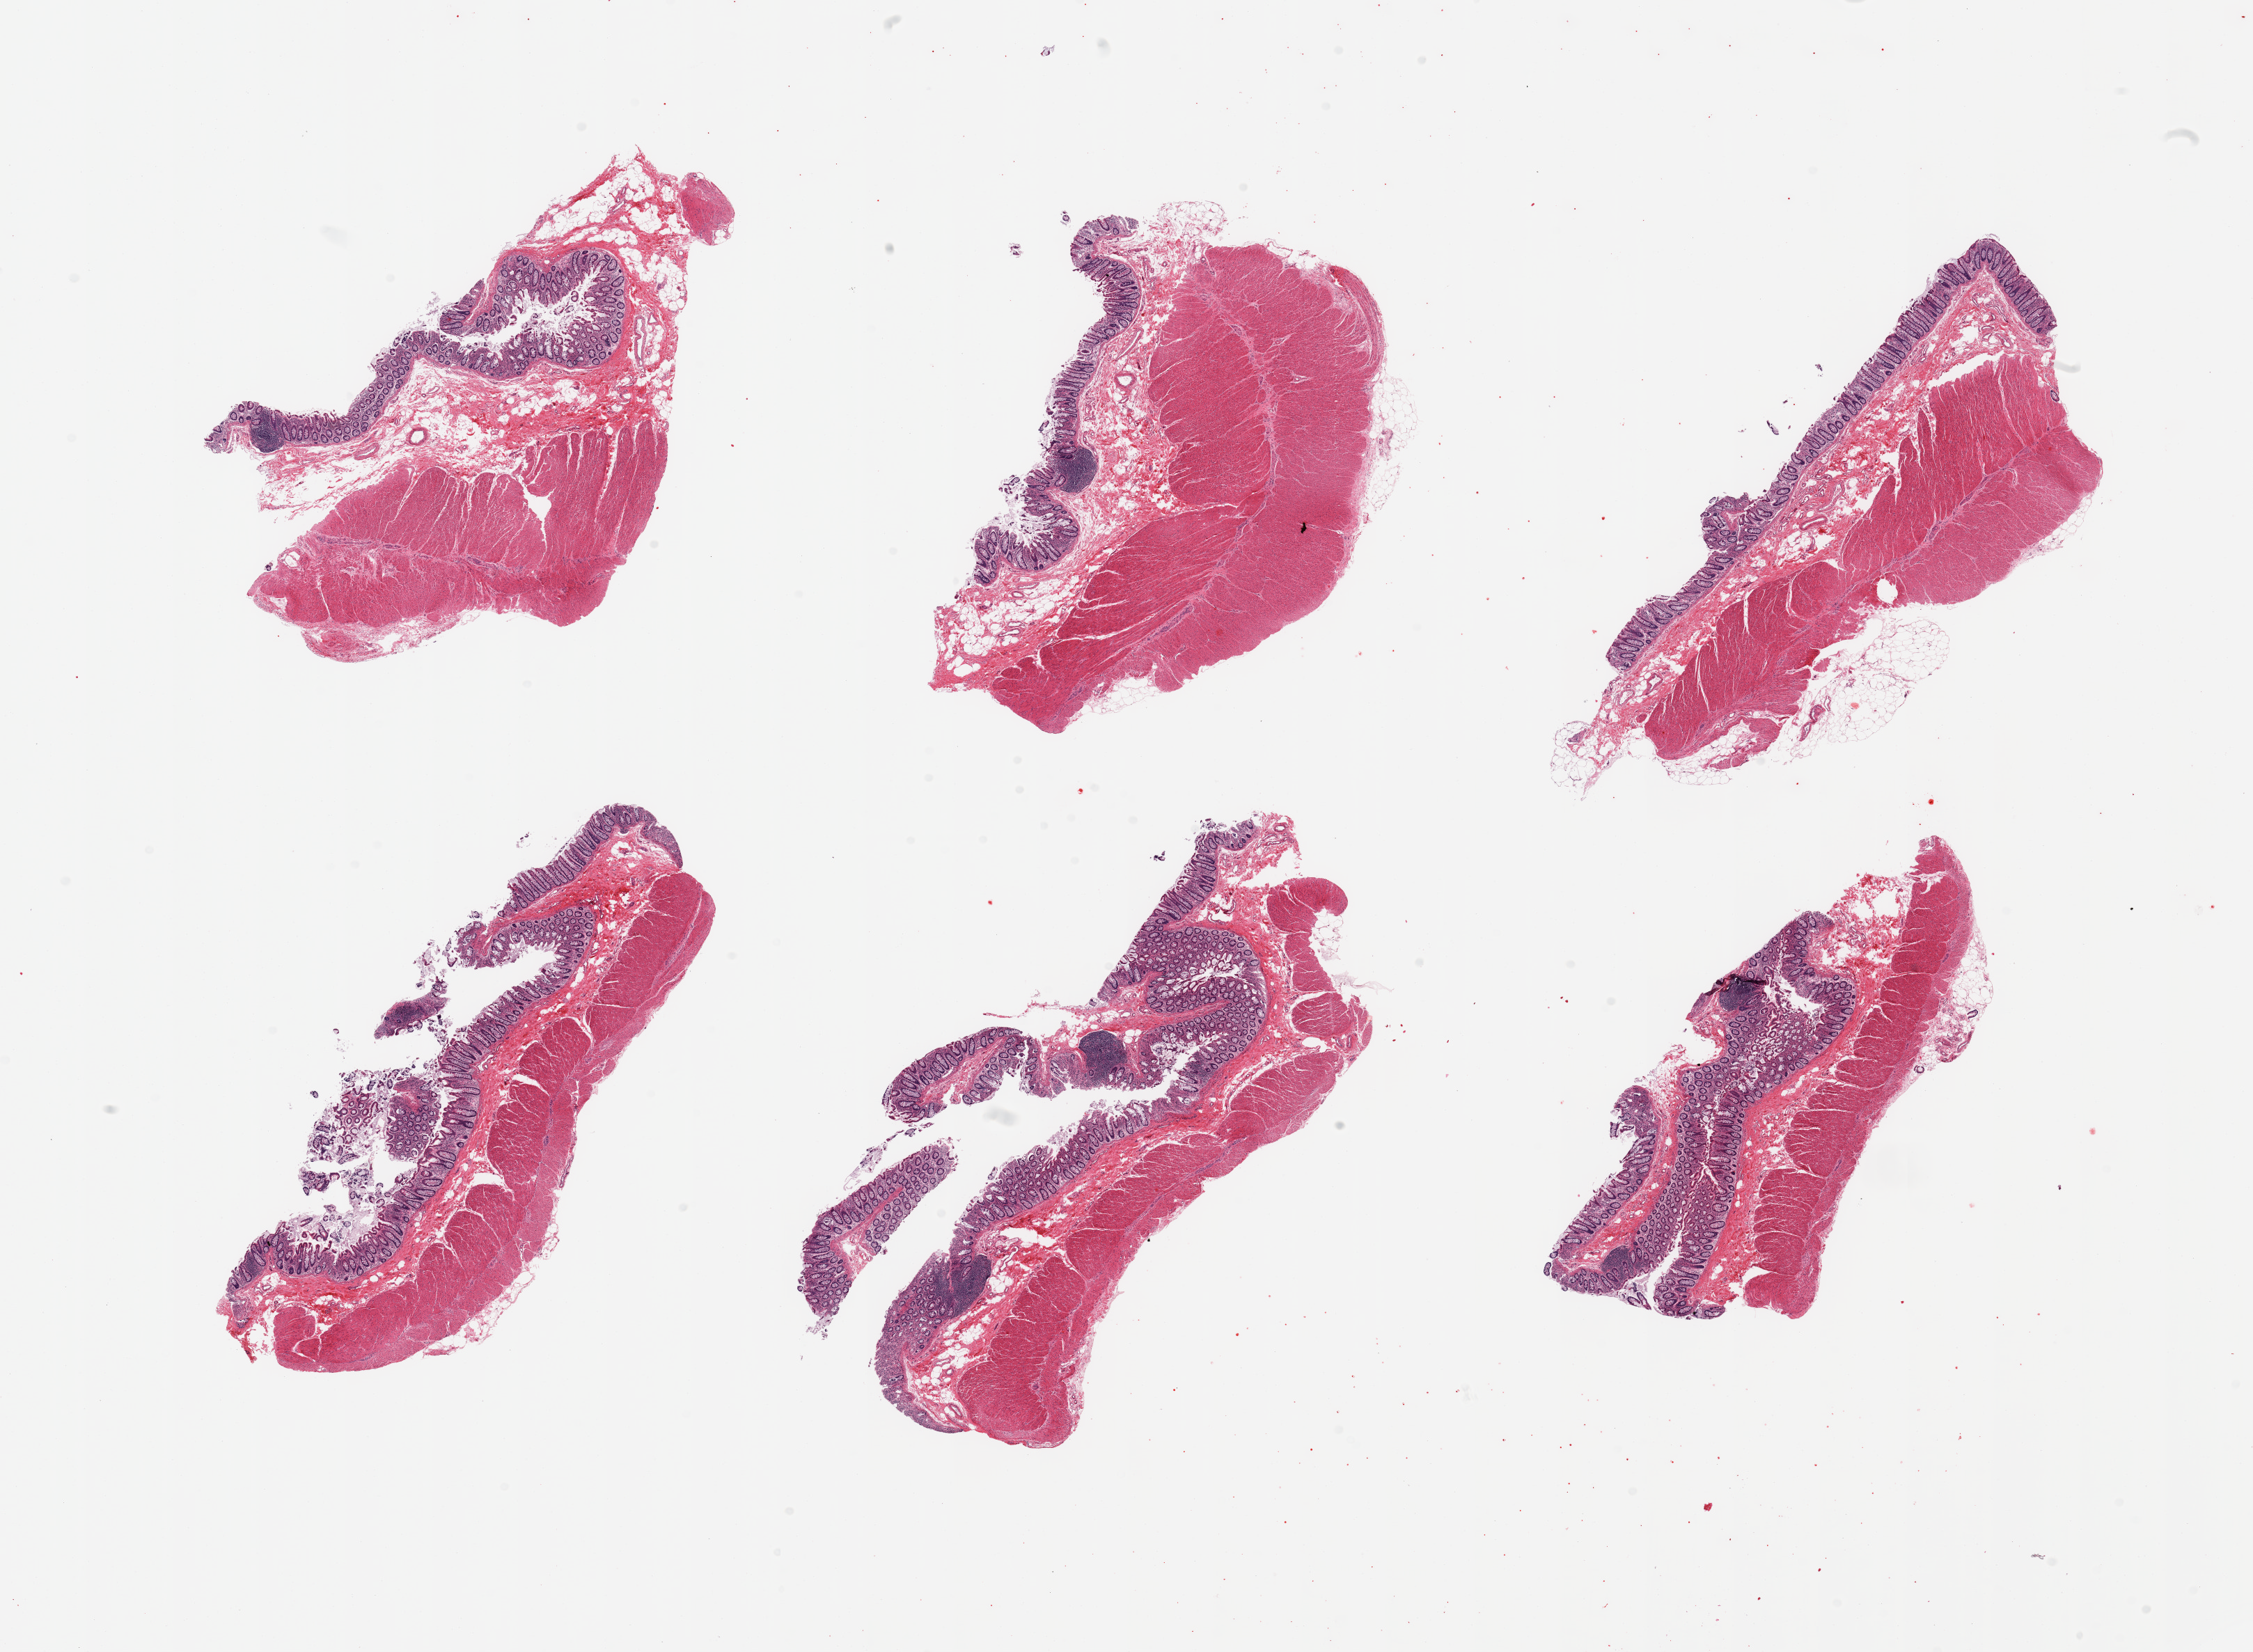
Whole-slide image, haematoxylin and eosin stain, whole scanned area (about 25.6 x 18.8 mm, slide scanned at 20x) shown as a low-resolution overview, PAXgene-fixed, paraffin-embedded tissue, sampled site (target tissue): transverse colon, donor tissue sample. Male donor.
Review note (as recorded): 6 pieces; full thickness sections, few with minimal attached fat.